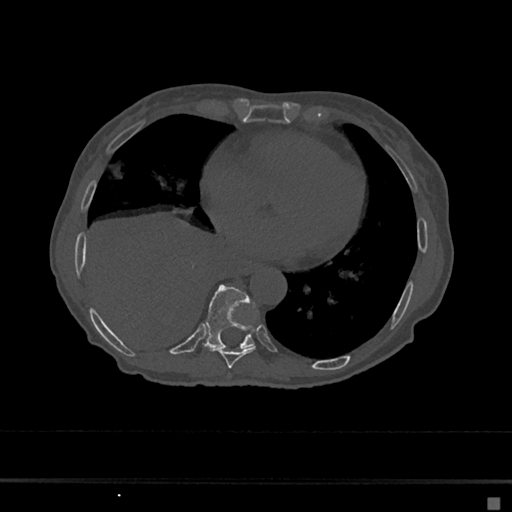
CT including the spine, one axial slice. Position 299 of 797 along the scan axis. Reconstruction kernel Br40s/3. 120 kVp. Bone window (W 1800 / L 400 HU). 0.5 mm slice thickness. 512 × 512 image matrix, field of view 360 × 360 mm. Female patient, age 68 years. Case-level facts recorded for this patient, not image findings: primary cancer: renal.
Outlined on this slice (semi-automatically segmented with operator editing):
- T8 vertebra: bounding box (x1, y1, x2, y2) in pixels: (210, 347, 256, 368)
- T9 vertebra: (203, 284, 255, 349)